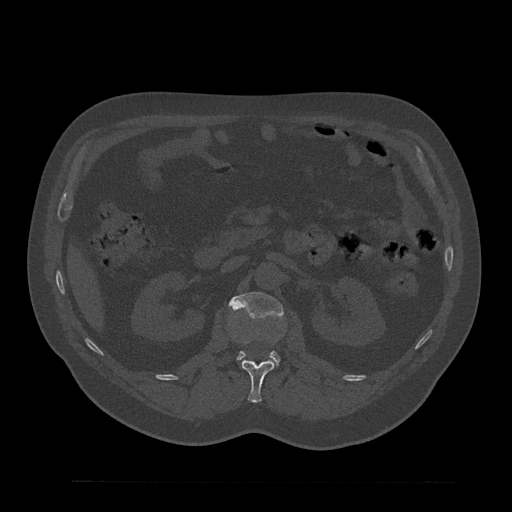
CT including the spine, one axial slice; position 138 of 797 along the scan axis; reconstruction kernel Br40s/3; 120 kVp; bone window (W 1800 / L 400 HU); 512 × 512 image matrix, field of view 430 × 430 mm. Patient: male, 61 years. From the clinical record (not read from this slice): primary cancer: prostate.
Structures marked on this image (semi-automatically segmented with operator editing):
- L1 vertebra: bounding box (x1, y1, x2, y2) in pixels: (233, 338, 275, 403)
- L2 vertebra: (228, 292, 283, 363)